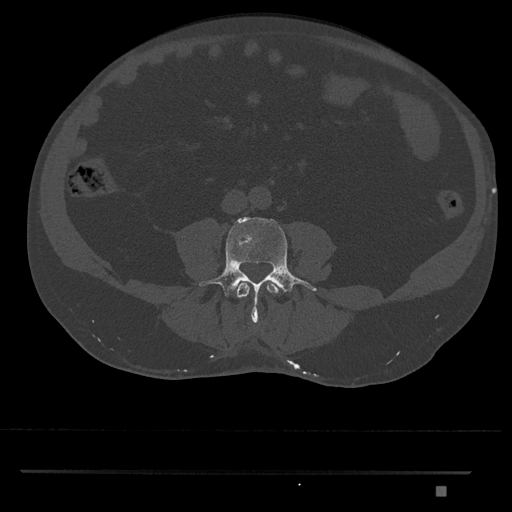
CT including the spine, one axial slice; slice 631 of 1134 in the series (ordered by position); reconstruction kernel Br40s/3; 120 kVp; bone window (W 1800 / L 400 HU); 0.5 mm slice thickness; 512 × 512 image matrix, field of view 429 × 429 mm. Male patient, age 65 years. From the clinical record (not read from this slice): primary cancer: prostate.
Annotated regions visible in this slice (semi-automatically segmented with operator editing):
- L3 vertebra: bounding box (x1, y1, x2, y2) in pixels: (236, 281, 279, 298)
- L4 vertebra: (199, 217, 316, 323)